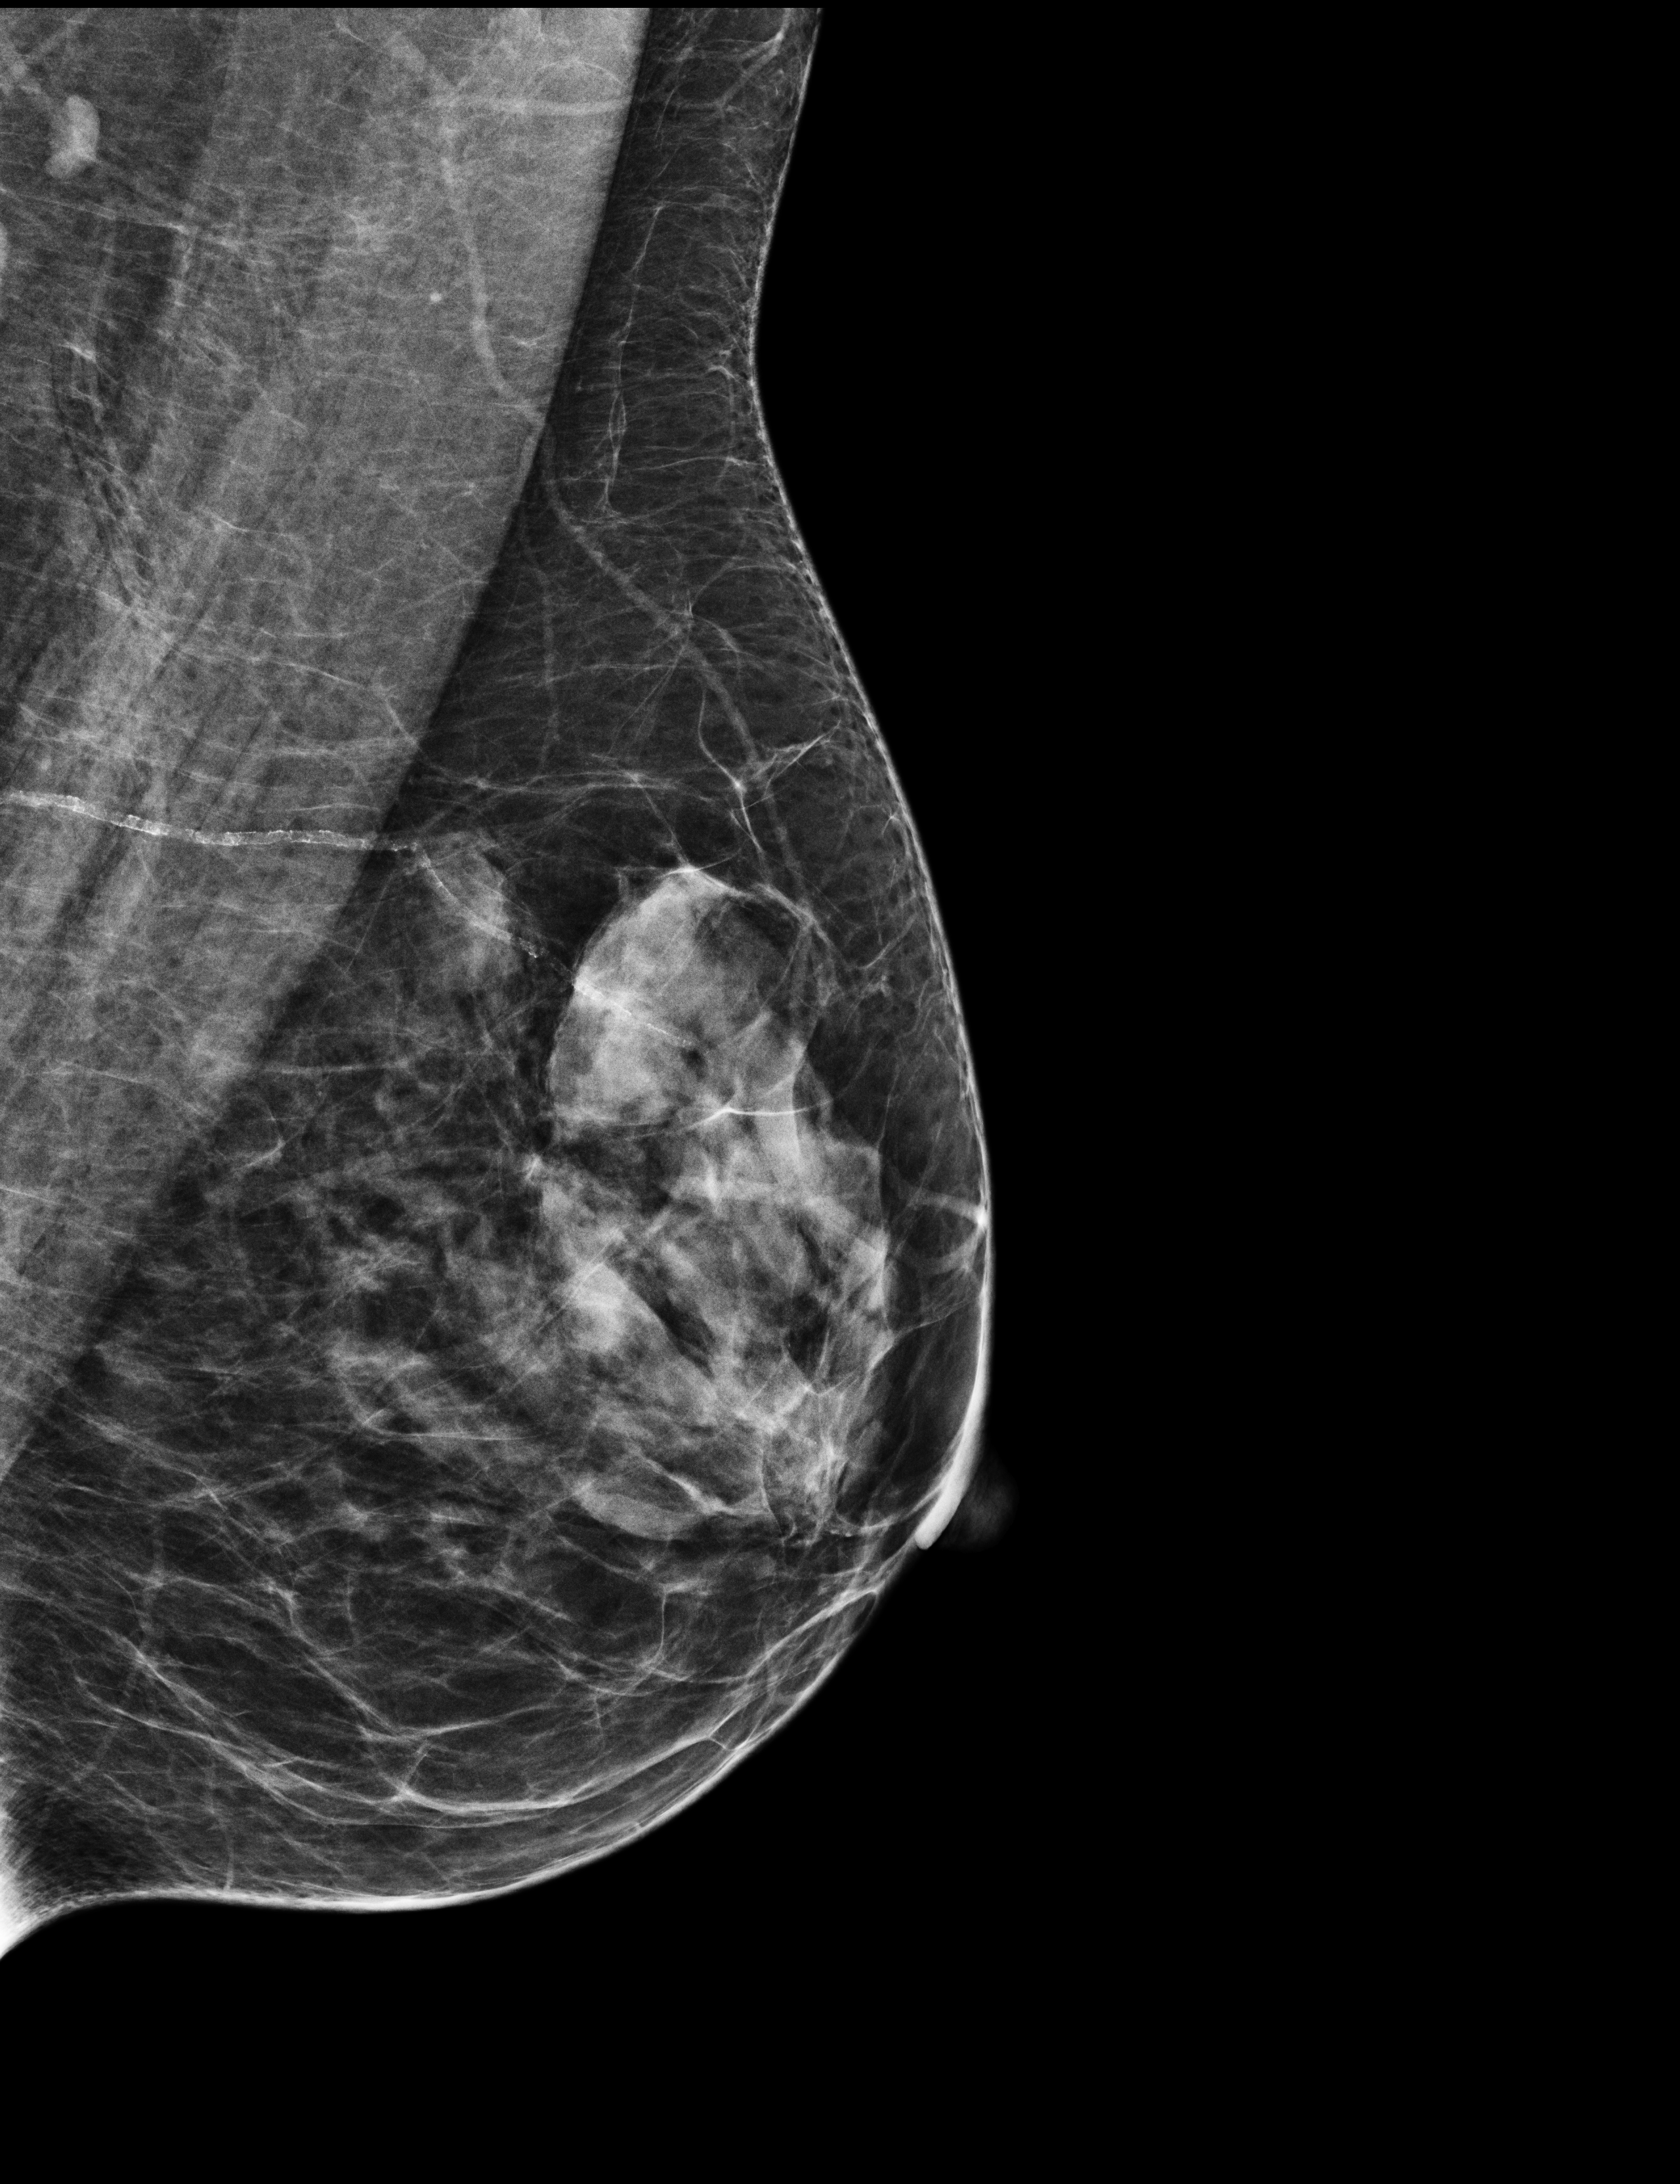
Screening examination, system: Selenia Dimensions. Female patient, age 58 years.
Image type: full-field digital mammogram. Breast: left. Projection: mediolateral oblique (MLO) view.